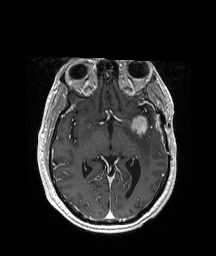
Brain MRI from a brain-tumour surgery series, one axial slice. Position 114 of 208 along the scan axis. T1-weighted post-contrast. 216 × 256 image matrix. Case-level facts recorded for this patient, not image findings: histopathology: Glioblastoma; WHO grade: 4.
Structures marked on this image (outlined manually by an expert reader):
- tumour: bounding box [x1, y1, x2, y2] px = [127, 115, 145, 133]